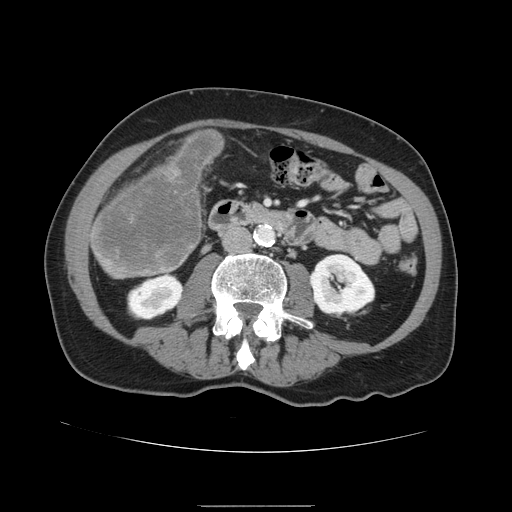
Contrast-enhanced abdominal CT, one axial slice. Position 34 of 168 along the scan axis. 120 kVp. Soft-tissue window (W 400 / L 40 HU). 2.5 mm slice thickness. 512 × 512 image matrix, field of view 386 × 386 mm. Male patient, age 74 years. Case-level facts recorded for this patient, not image findings: diagnosis: colorectal cancer liver metastases, imaged before liver resection; multiple liver metastases: no; largest metastasis: 14.5 cm; disease in both lobes: yes.
Outlined on this slice (manually delineated by an expert):
- liver: box from (x=90, y=130) to (x=225, y=279) px
- liver metastasis: (x=94, y=131)–(x=223, y=274)